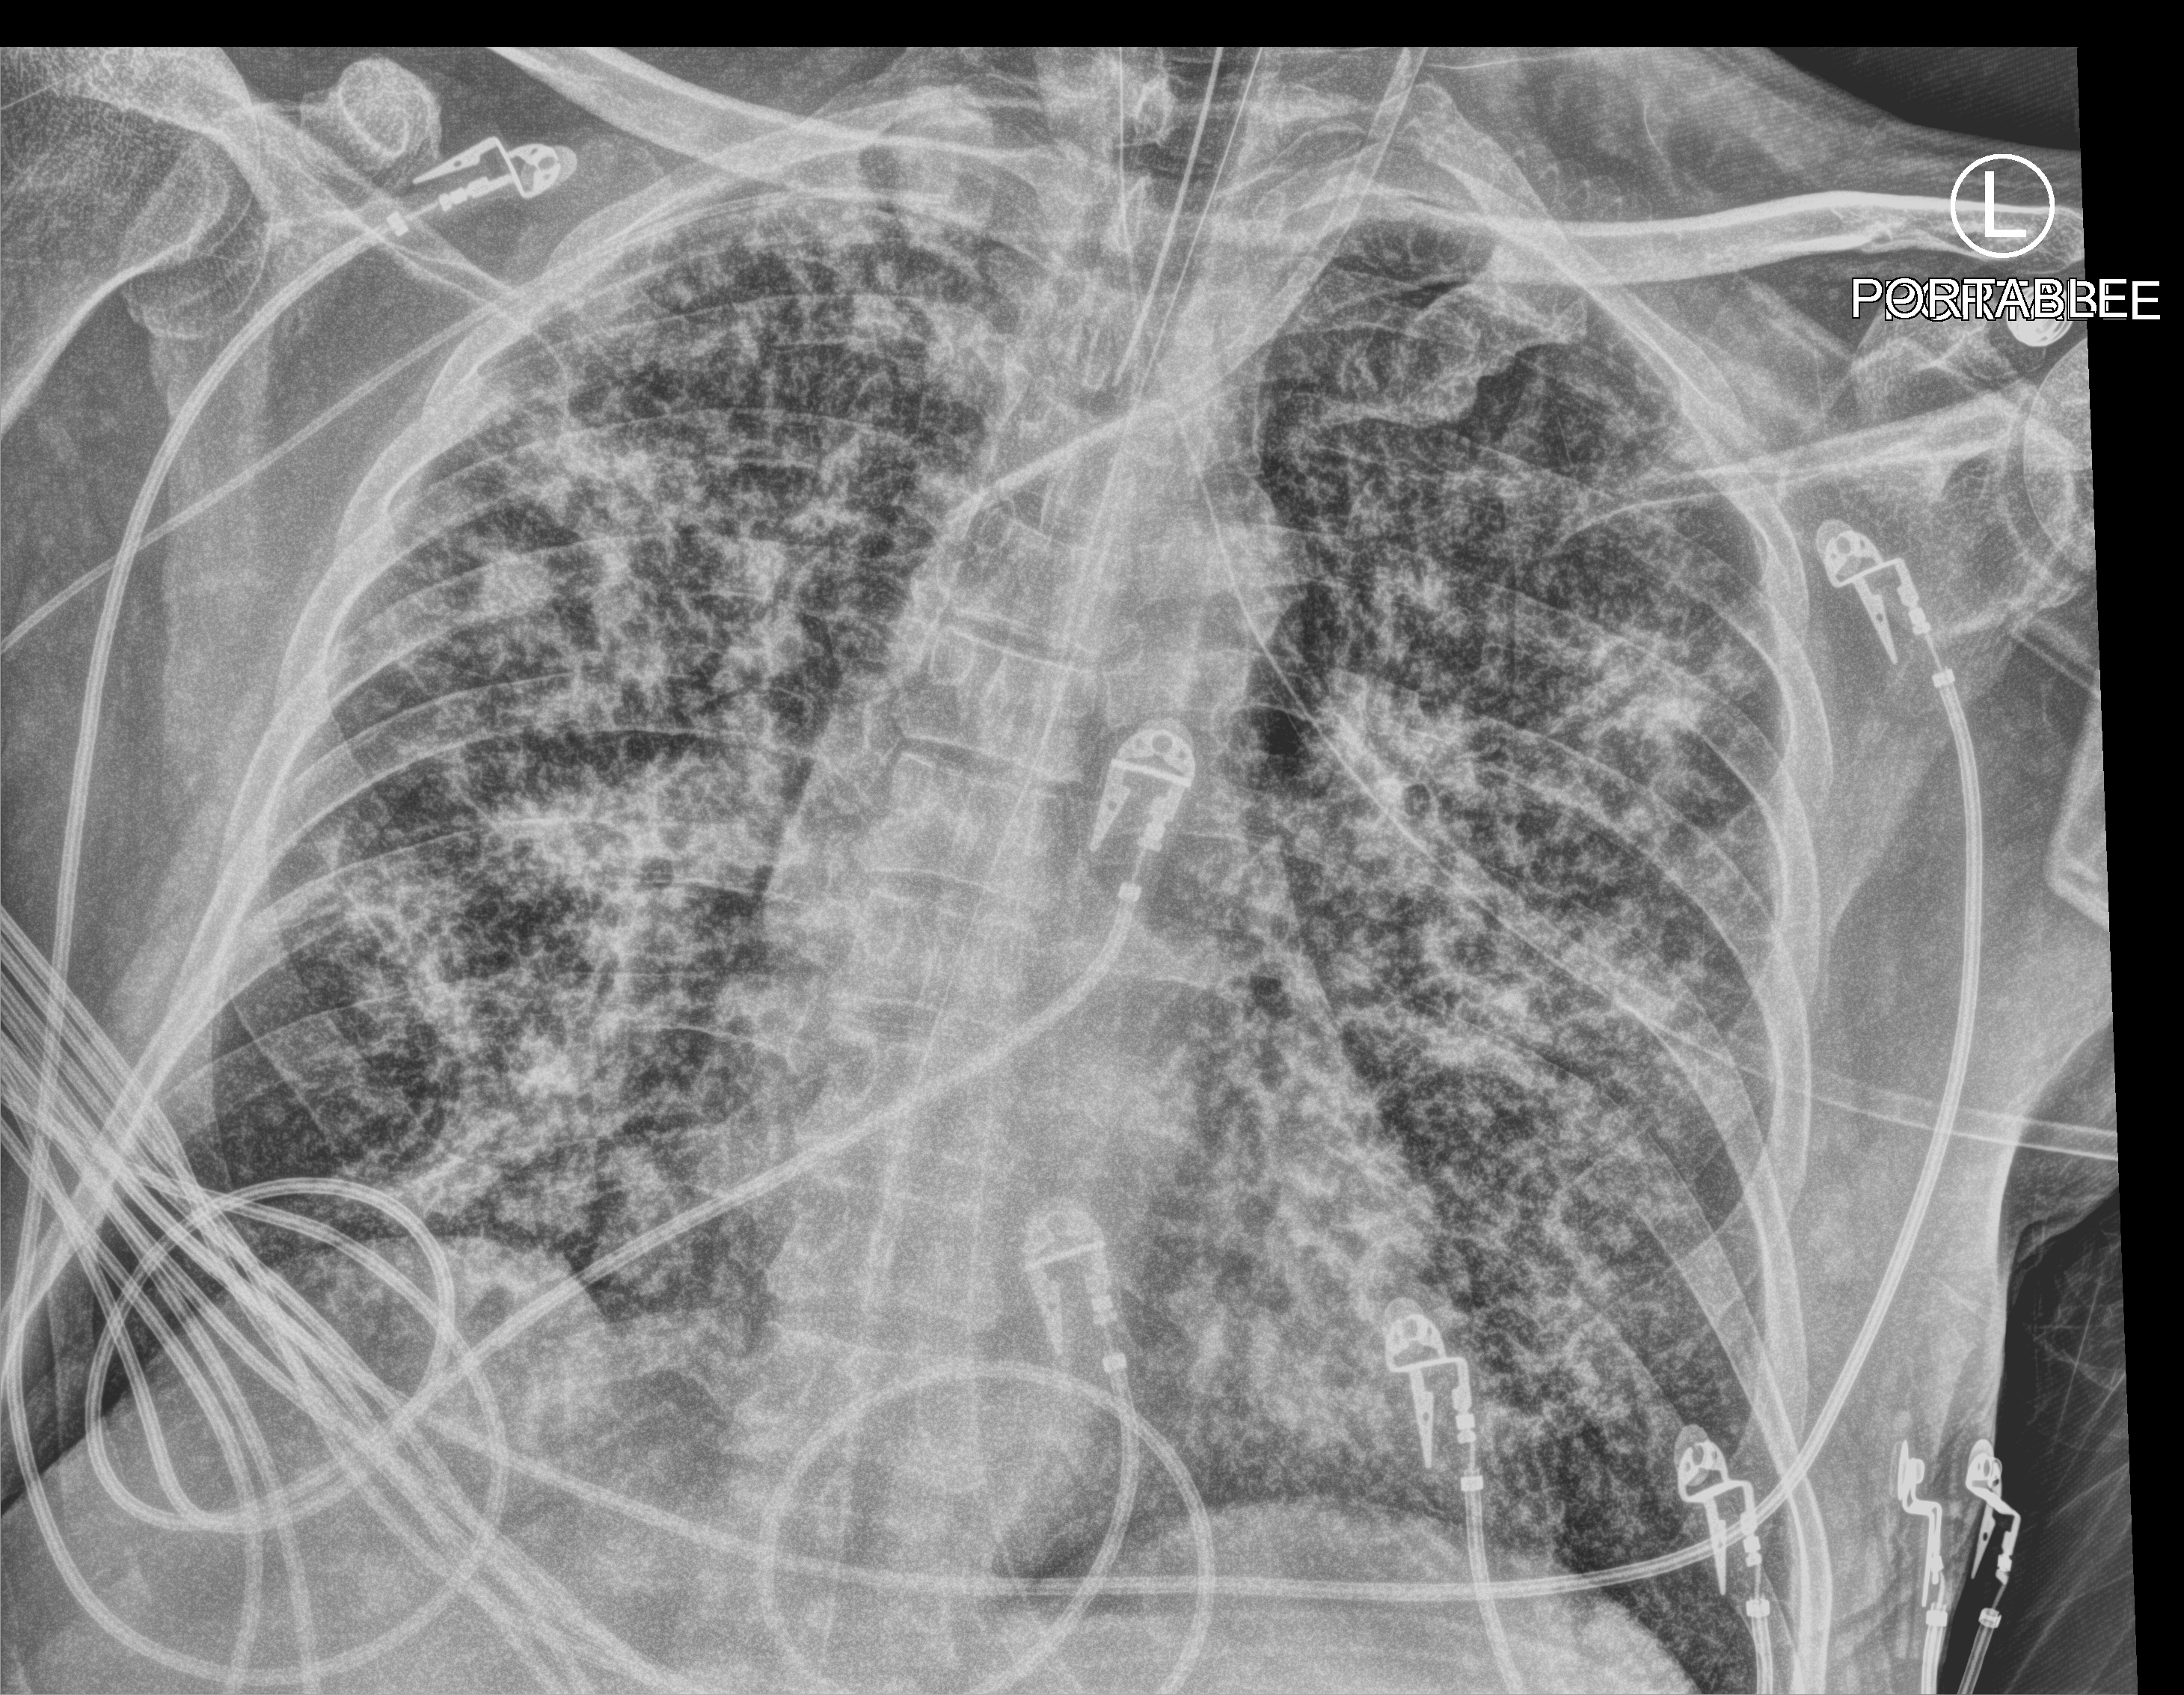
Chest X-ray (portable); anteroposterior (AP) projection. Male patient hospitalised with COVID-19, age 60–74 years.
Admission-level facts for this patient (not findings on this image; timing relative to this image not recorded): admitted to intensive care during this hospital stay: yes; mechanically ventilated during this hospital stay: yes.